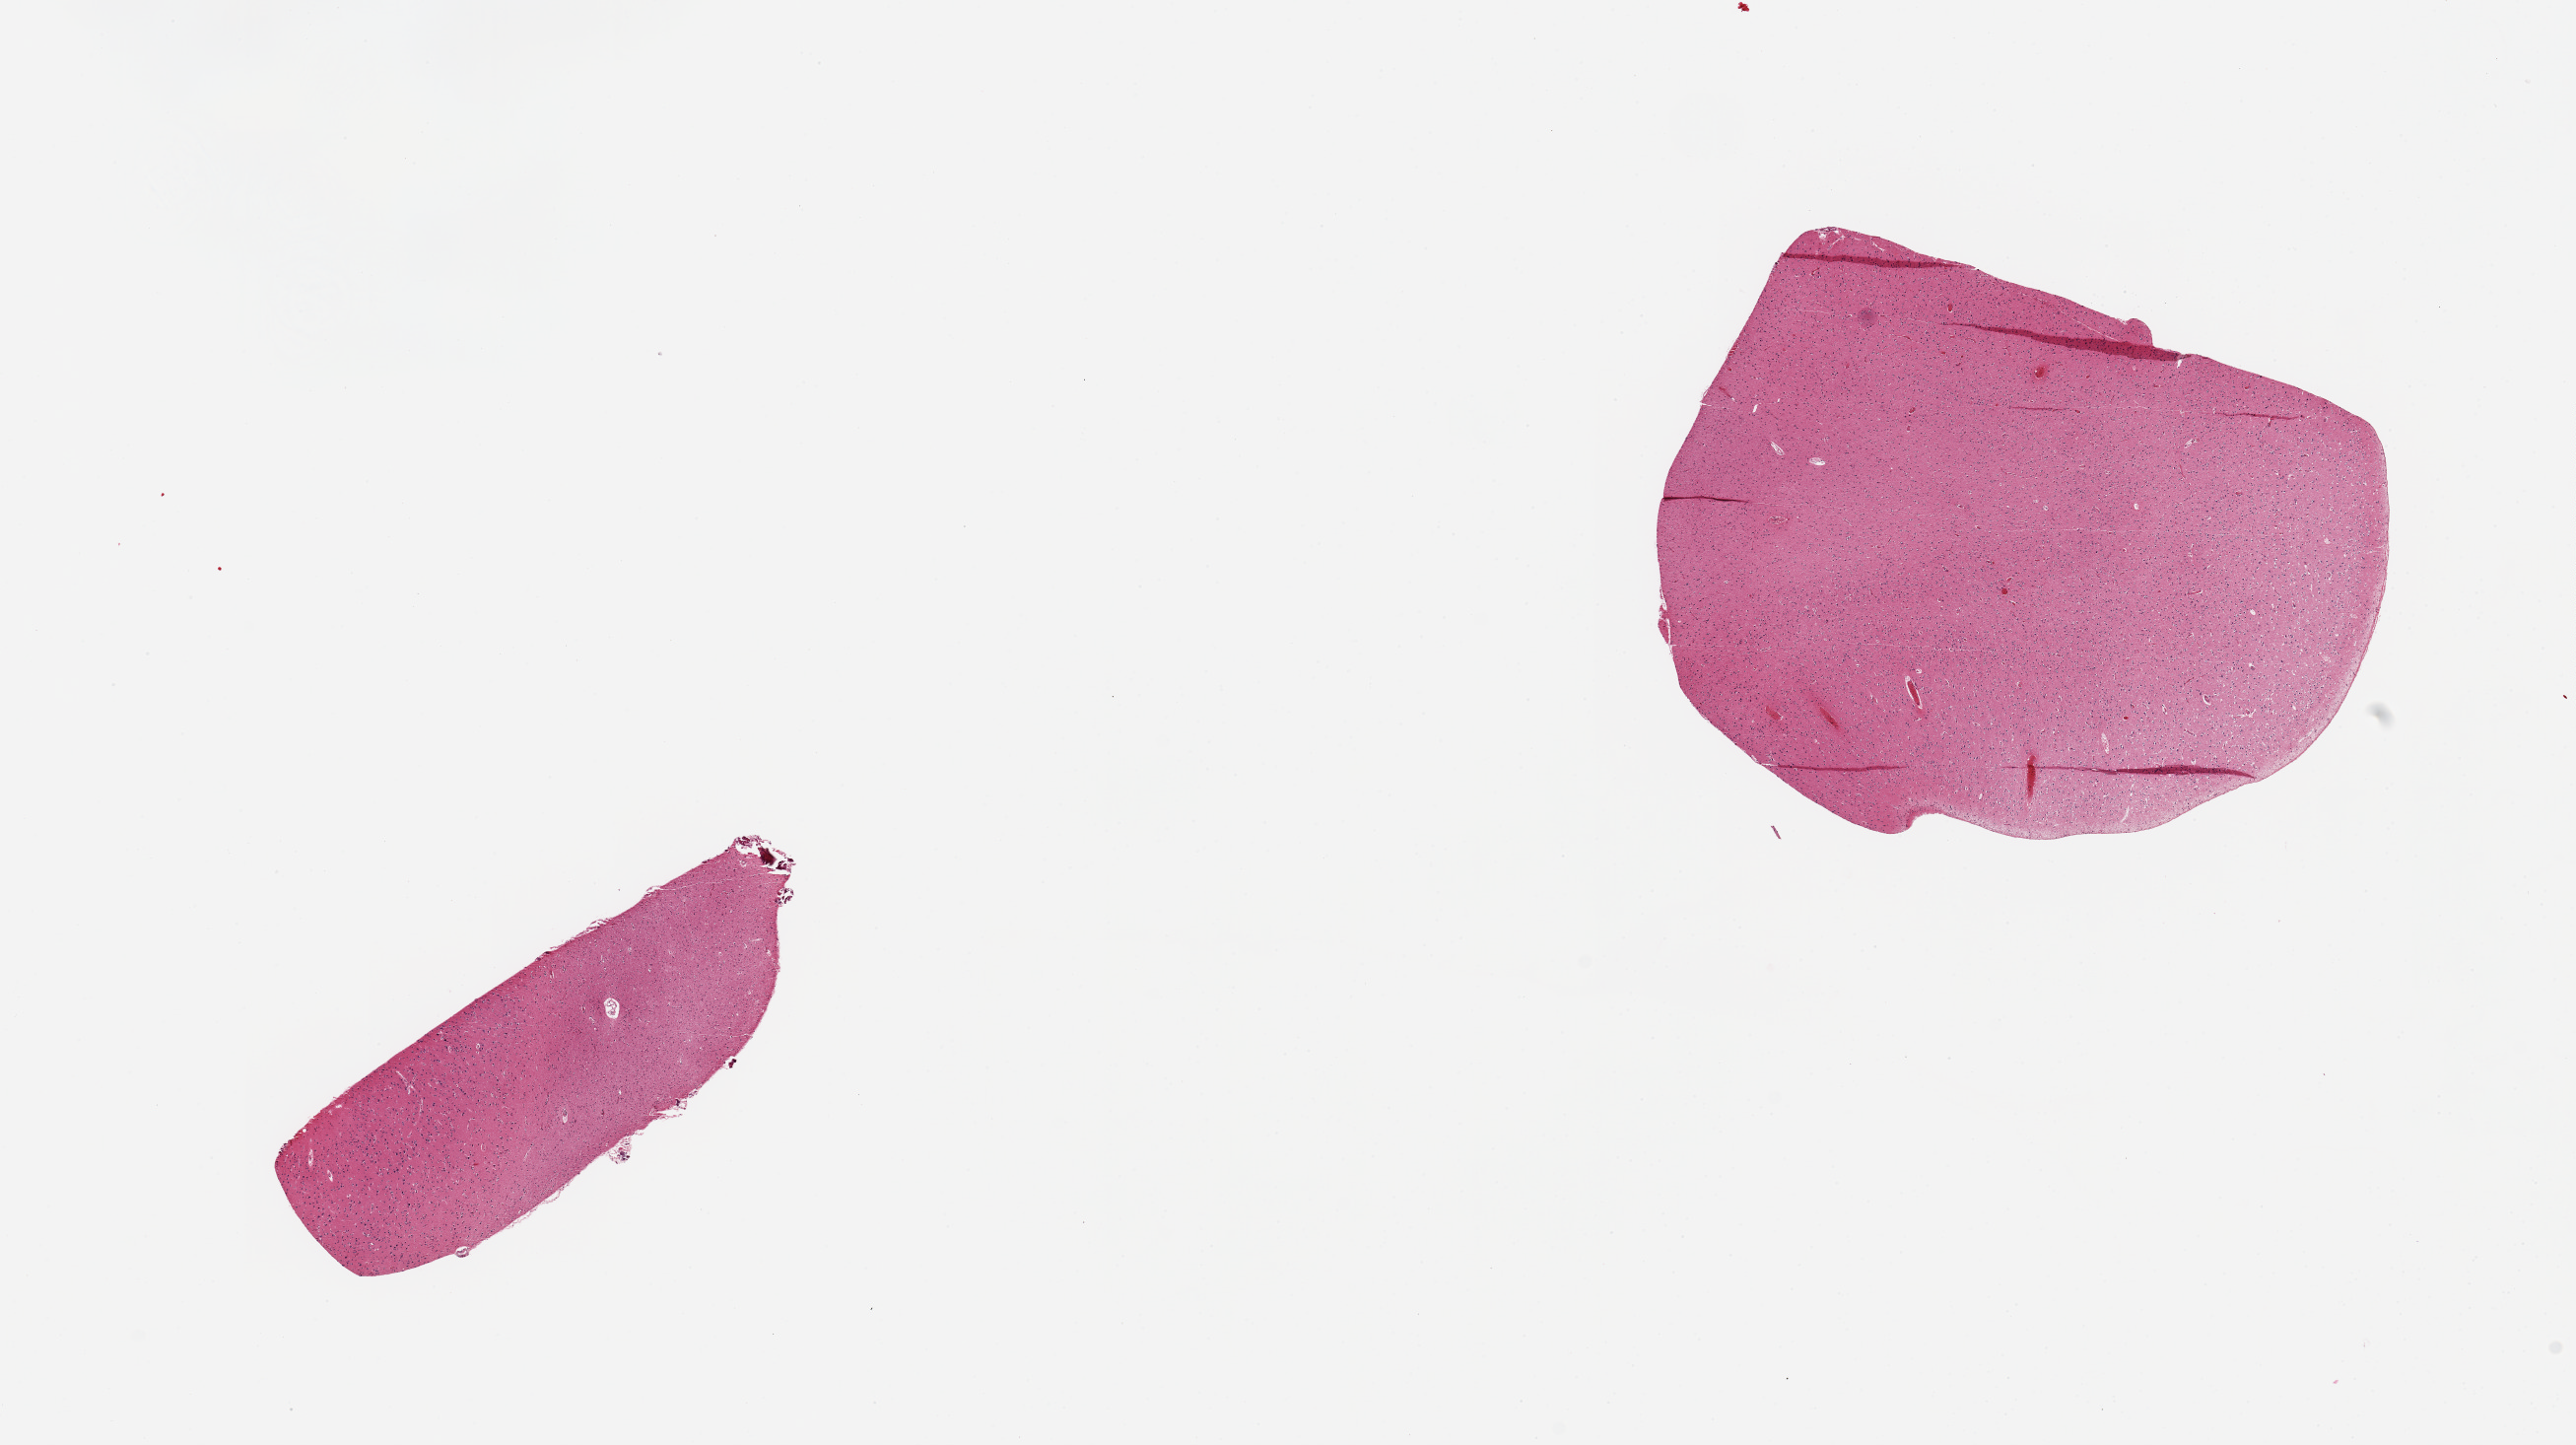
Digitized H&E-stained section — low-resolution overview of the scanned area, about 20.7 x 11.6 mm (slide scanned at 20x); PAXgene-fixed, paraffin-embedded tissue; sampled site (target tissue): cerebral cortex; tissue donor sample.
Reviewer comment on this tissue sample: 2 pieces; target is 4.